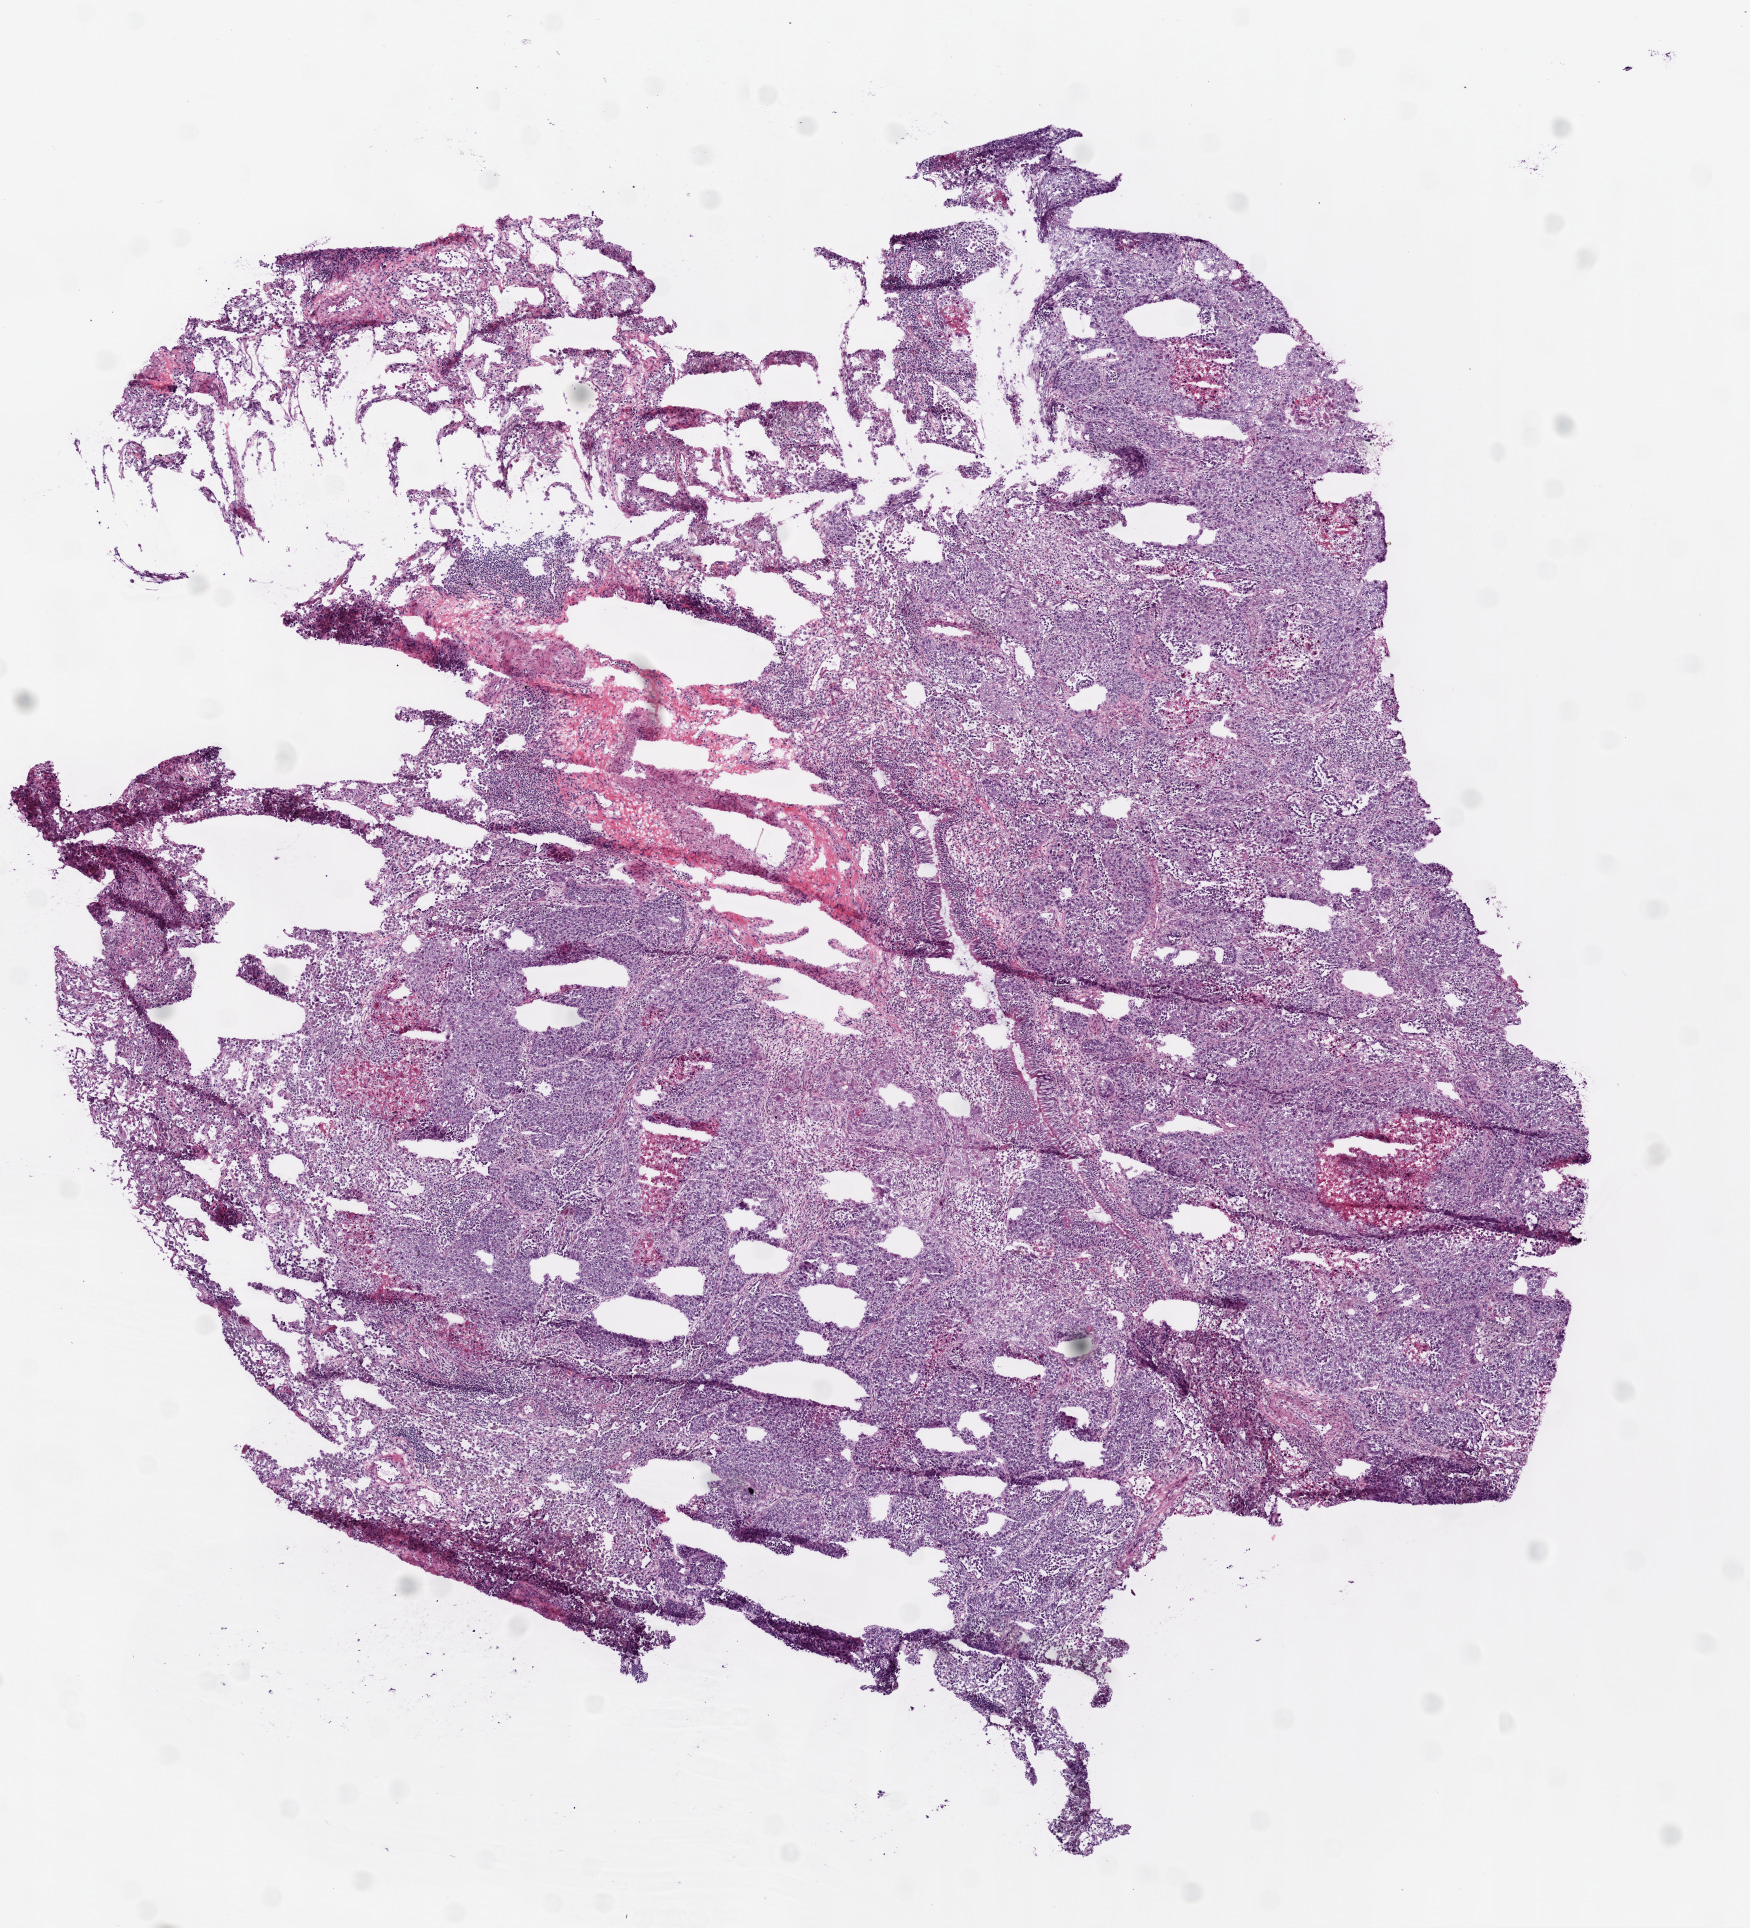
Whole-slide histology image, Hematoxylin and eosin (H&E) stained — whole scanned area (about 7.0 x 7.7 mm, acquisition: 20x scan) shown as a low-resolution overview, frozen section from the top of the tissue portion, sample: primary tumour, lung. Male patient; age at initial diagnosis 71 years. Pathologist review of this section (percent, as recorded): tumour cells 80%, tumour nuclei 50%, normal cells 10%, stromal cells 5%, necrosis 5%. Infiltration values recorded for this section: lymphocyte infiltration 40%, monocyte infiltration 3%, neutrophil infiltration 0%.
* pathologic diagnosis: Squamous cell carcinoma, NOS
* AJCC pathologic stage: IB (6th edition)
* laterality: right